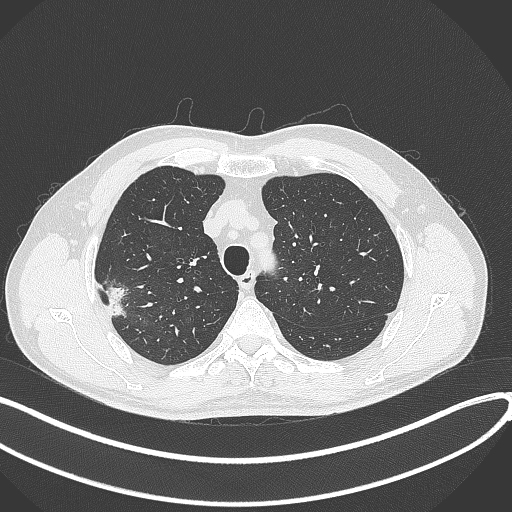
Chest CT, one axial slice; slice 328 of 381 in the series (ordered by position); lung window (W 1500 / L -600 HU); 1 mm slice thickness; 512 × 512 image matrix, field of view 400 × 400 mm. Male patient, age 62 years. From the clinical record (not read from this slice): clinical TNM (as recorded): T1c N0 M0.
Structures marked on this image (bounding box drawn by a radiologist):
- lung tumour (recorded histology: adenocarcinoma): bounding box <101,283,128,318> (left, top, right, bottom; pixels)